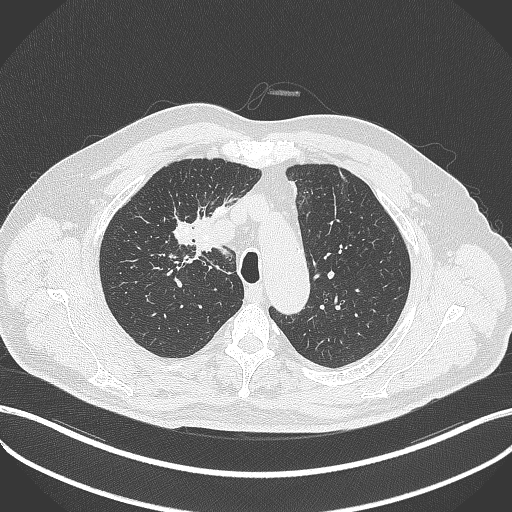
Chest CT, one axial slice; slice 300 of 411 in the series (ordered by position); reconstruction kernel B70f; 120 kVp; lung window (W 1500 / L -600 HU); 1 mm slice thickness; 512 × 512 image matrix. Patient: male, 60 years. From the clinical record (not read from this slice): clinical TNM (as recorded): T1b N1 M0.
Annotated regions visible in this slice (rectangle marked by the reading radiologist):
- lung tumour (recorded histology: squamous cell carcinoma): bounding box [x1, y1, x2, y2] px = [192, 218, 216, 254]